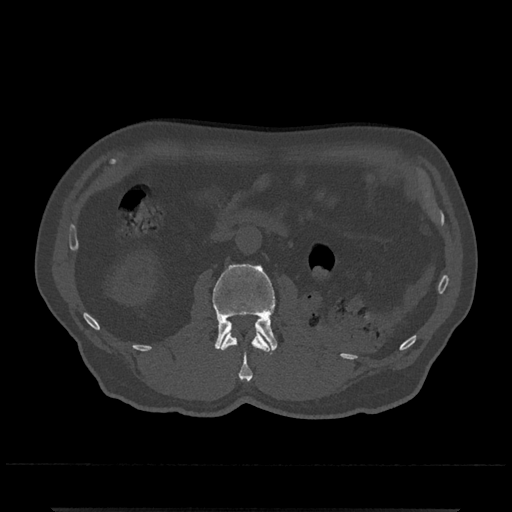
CT including the spine, one axial slice. 120 kVp. Bone window (W 1800 / L 400 HU). 0.5 mm slice thickness. 512 × 512 image matrix, field of view 393 × 393 mm. Patient: male, 67 years. Case-level facts recorded for this patient, not image findings: primary cancer: prostate.
Structures marked on this image (semi-automatic segmentation, software-assisted and operator-edited):
- L1 vertebra: box from (x=221, y=330) to (x=270, y=381) px
- L2 vertebra: (x=212, y=264)–(x=278, y=353)